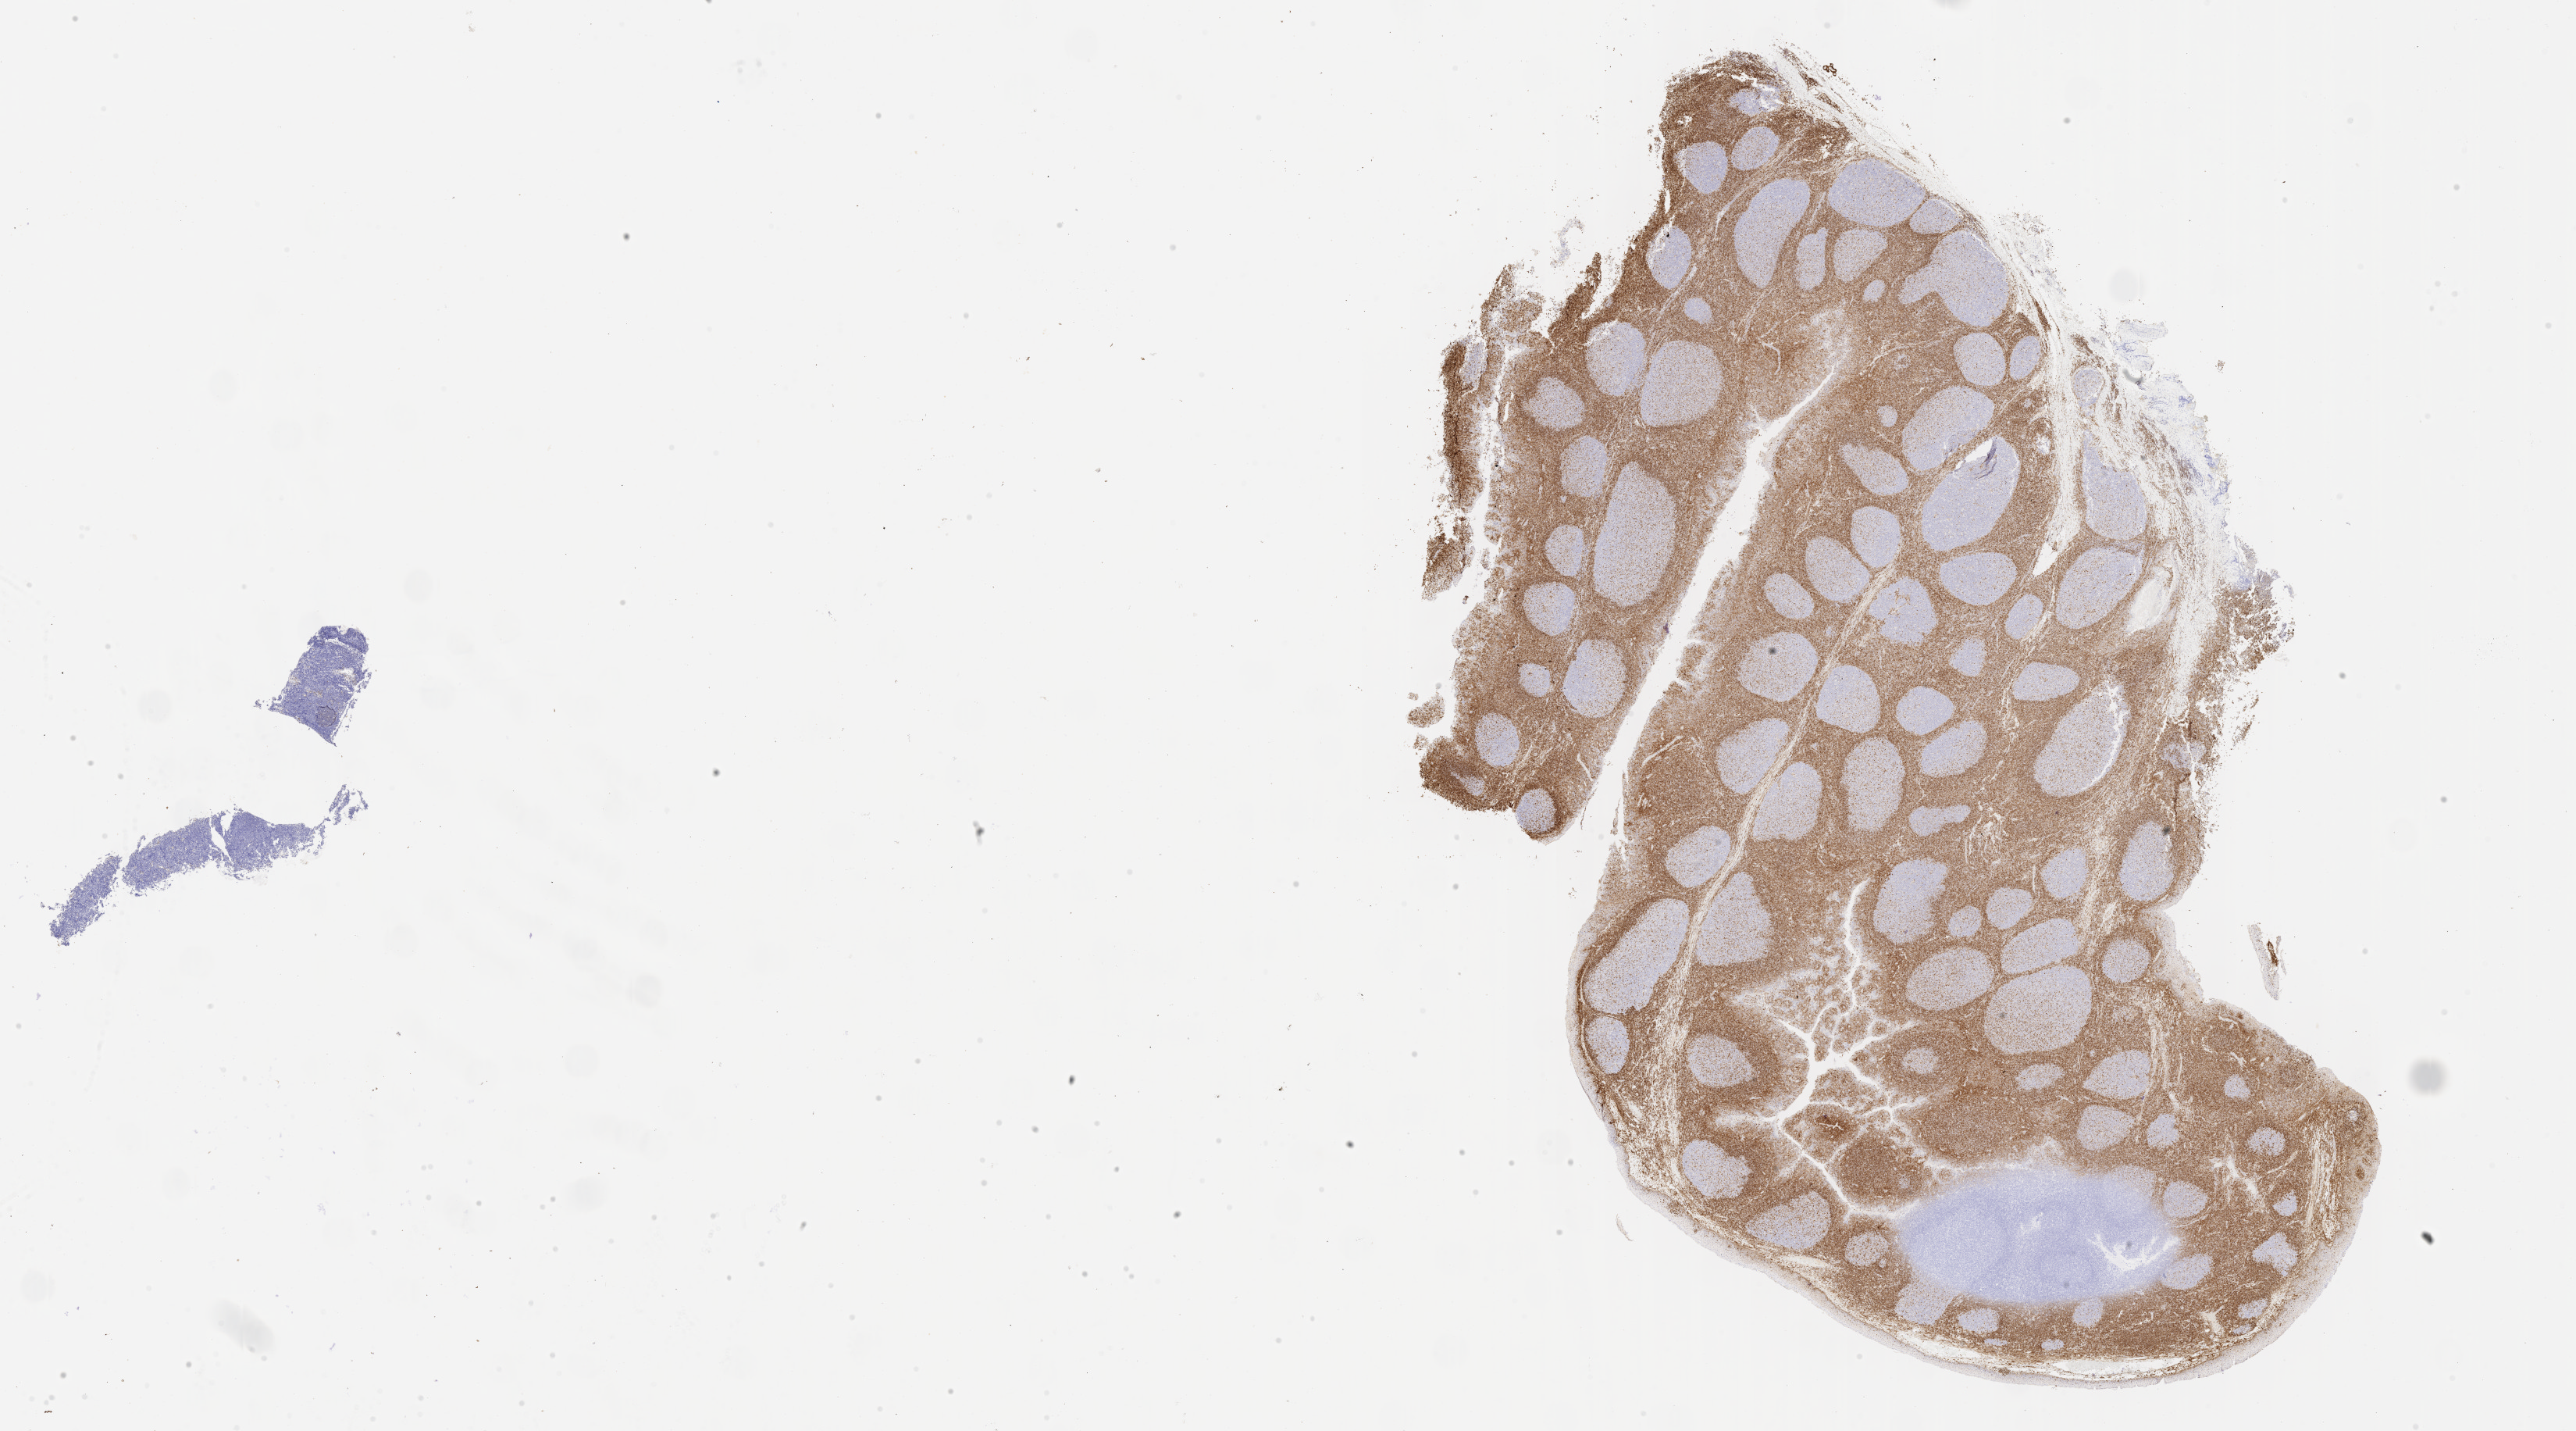
Whole-slide image, immunohistochemical stain for BCL2 — whole scanned area (about 26.7 x 14.8 mm) shown as a low-resolution overview, tumor tissue, site: cranium. Male, age 6 years at initial diagnosis.
Histologic diagnosis: Burkitt lymphoma, NOS.